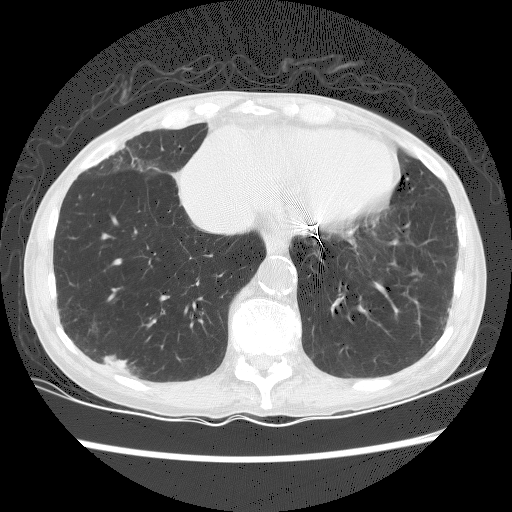
Low-dose screening chest CT, one axial slice; slice 57 of 156 in the series (ordered by position); 120 kVp; lung window (W 1500 / L -600 HU); 2.5 mm slice thickness; 512 × 512 image matrix, field of view 320 × 320 mm.
Structures marked on this image (expert manual segmentation):
- lesion 1 (tumor, lower lobe of right lung): box from (x=103, y=355) to (x=135, y=371) px